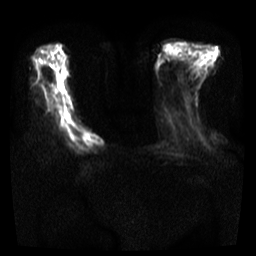
Breast MRI, one axial slice. Position 10 of 35 along the scan axis. Diffusion-weighted series; image 2 of 4 stored at this slice position (different b-values; order by instance number). 3 T. 5 mm slice thickness. 256 × 256 image matrix. Female patient.
Annotated regions visible in this slice (outlined manually by an expert reader):
- tumour on diffusion-weighted imaging: bounding box [x1, y1, x2, y2] px = [80, 129, 106, 148]